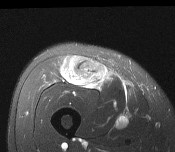
MRI of an extremity soft-tissue mass, one axial slice; T2-weighted fat-saturated; MR volume resampled by the dataset authors to the PET/CT grid (not the native acquisition matrix); 175 × 152 image matrix. Male patient. Case-level facts recorded for this patient, not image findings: histological type: pleiomorphic leiomyosarcoma; grade: intermediate; site of the primary tumour: right thigh.
Structures marked on this image (expert contour drawn on MRI and transferred to this co-registered scan by the dataset authors):
- gross tumour volume including surrounding oedema: bounding box [x1, y1, x2, y2] px = [60, 56, 107, 87]